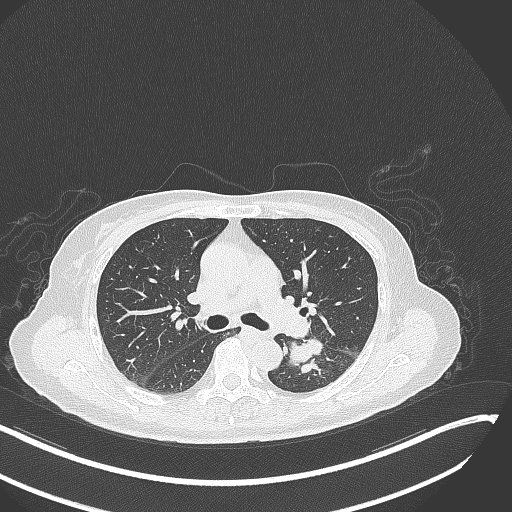
Chest CT, one axial slice; slice 175 of 342 in the series (ordered by position); reconstruction kernel B70f; 120 kVp; lung window (W 1500 / L -600 HU); 1 mm slice thickness; 512 × 512 image matrix. Patient: female, 64 years. From the clinical record (not read from this slice): clinical TNM (as recorded): T3 N1 M1; histopathological grade: G3.
Structures marked on this image (rectangle marked by the reading radiologist):
- lung tumour (recorded histology: small cell carcinoma): bounding box (x1, y1, x2, y2) in pixels: (290, 335, 326, 375)